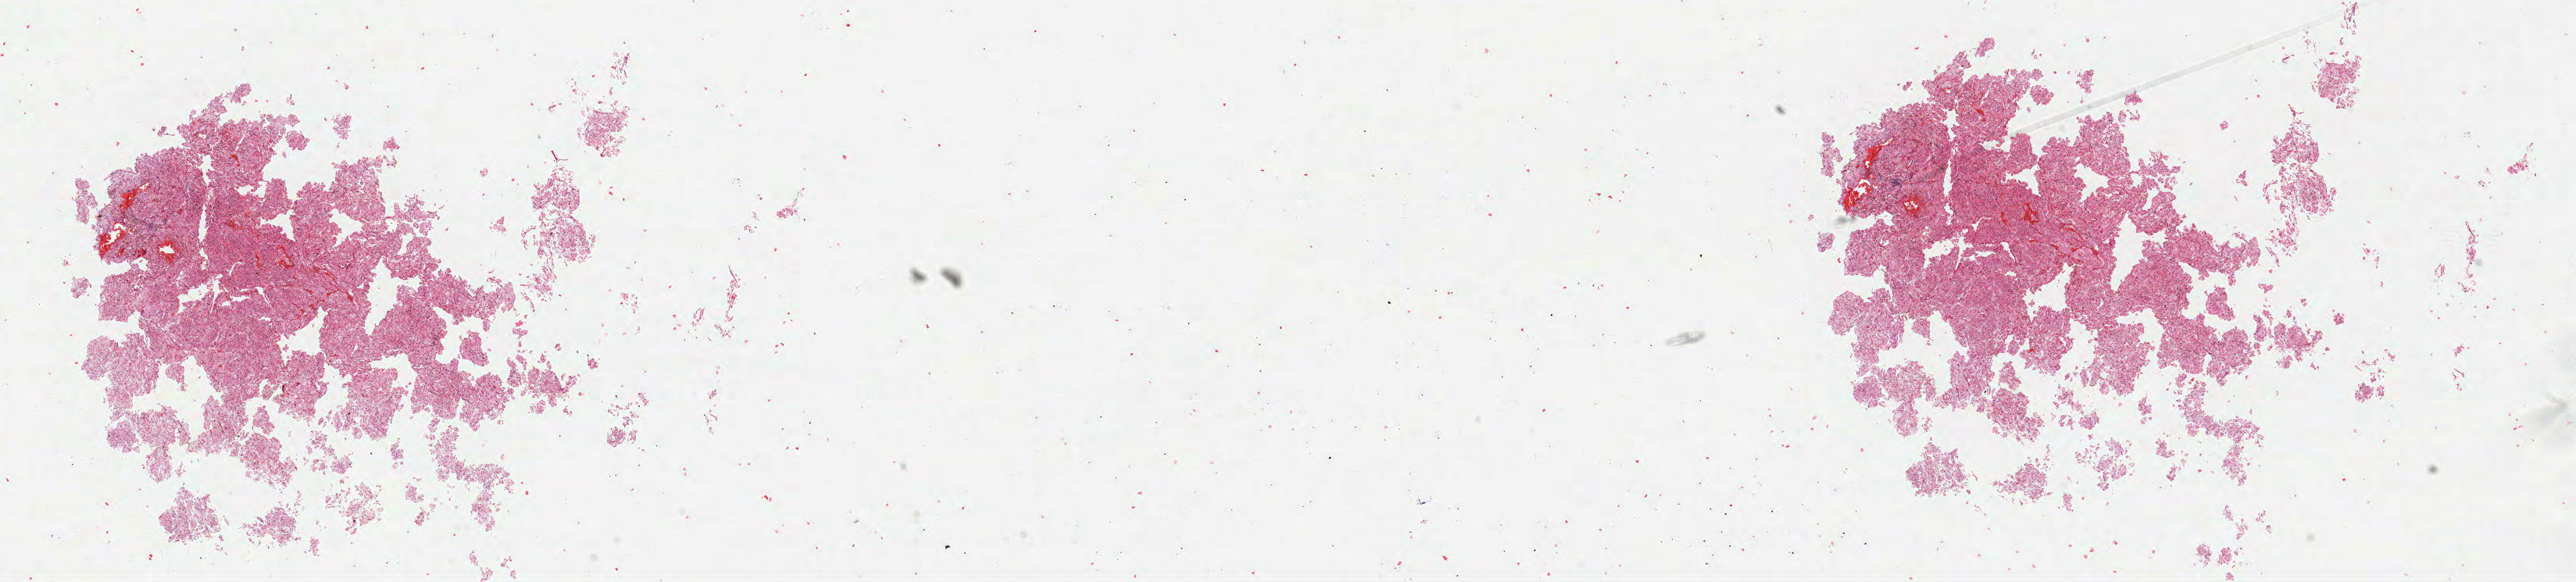
Whole-slide histology image, Hematoxylin and eosin (H&E) stained — shown as a low-resolution overview of the whole scanned area (about 26.6 x 6.0 mm, slide scanned at 40x), formalin-fixed paraffin-embedded (FFPE) diagnostic section, primary tumour sample from the kidney. Male, age 63 years at initial diagnosis.
- diagnosis: Clear cell adenocarcinoma, NOS
- AJCC pathologic stage: I
- TNM: T1a NX M0